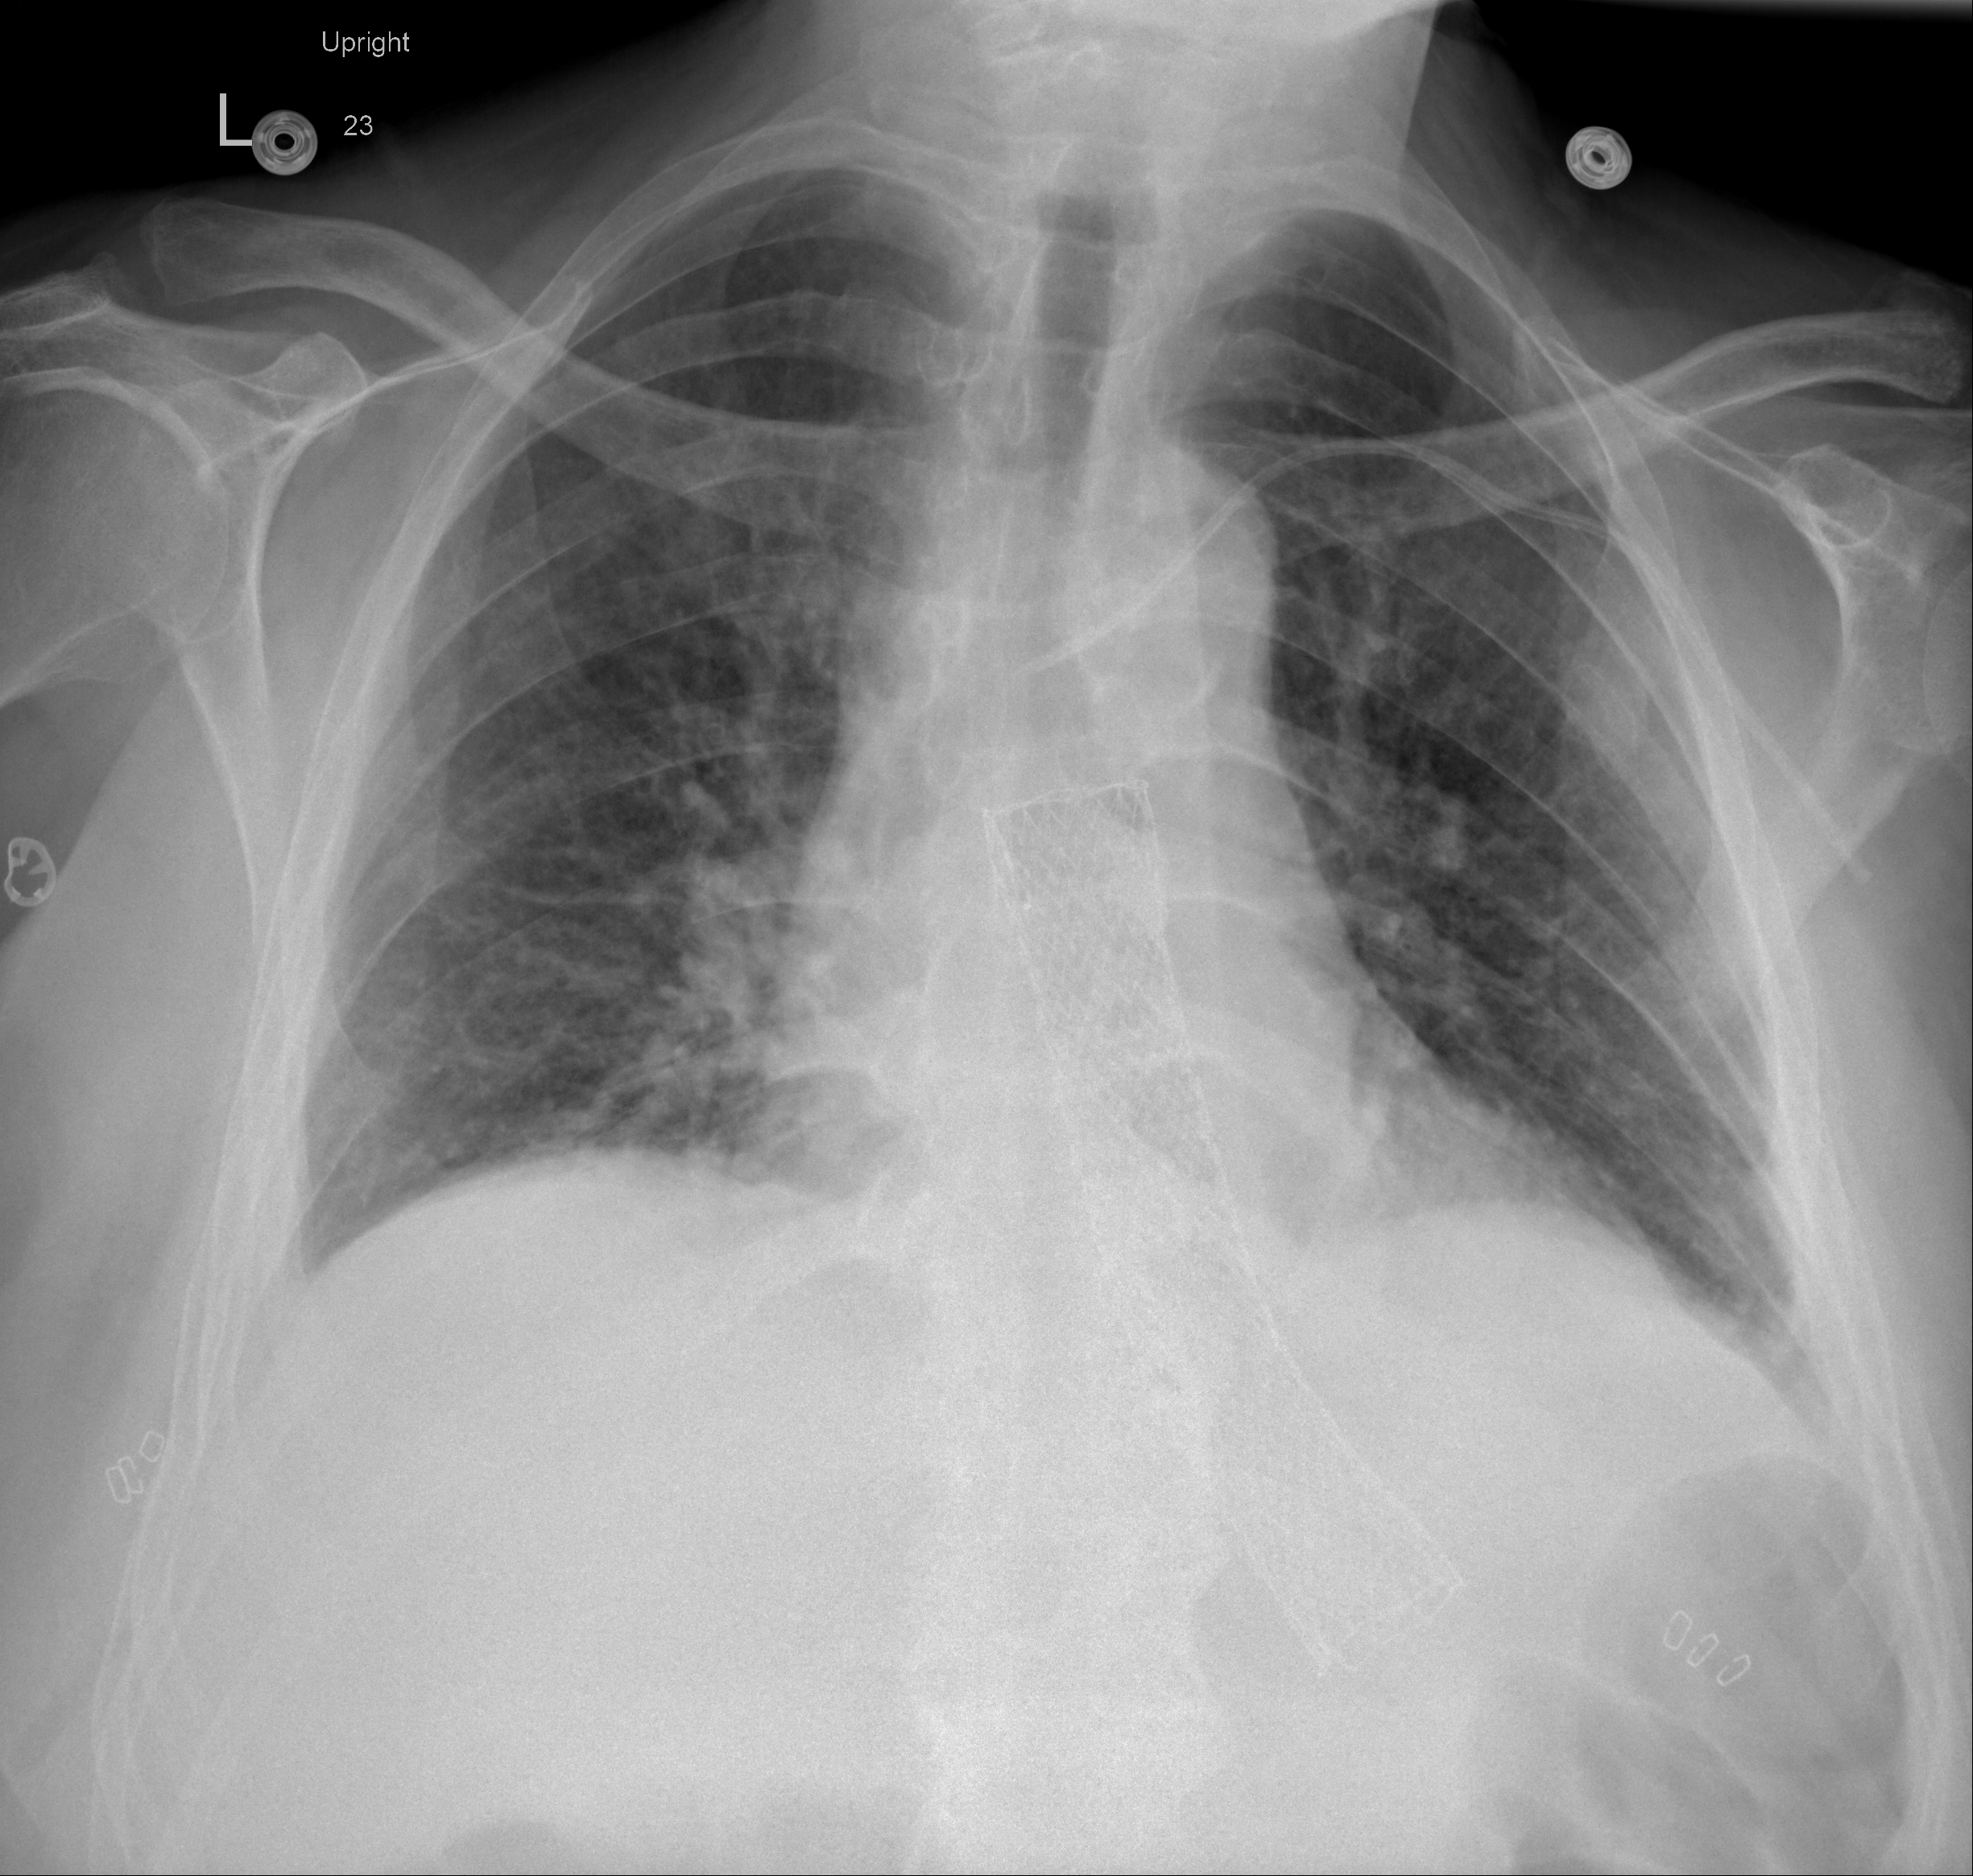
Portable chest radiograph, AP projection. Male patient, age 64 years; imaged 13 days after the COVID-19 diagnosis.
Key findings recorded by the radiologist: Trace bilateral pleural effusions/pleural thickening. Mild bibasilar atelectatic changes. No superimposed airspace consolidation.